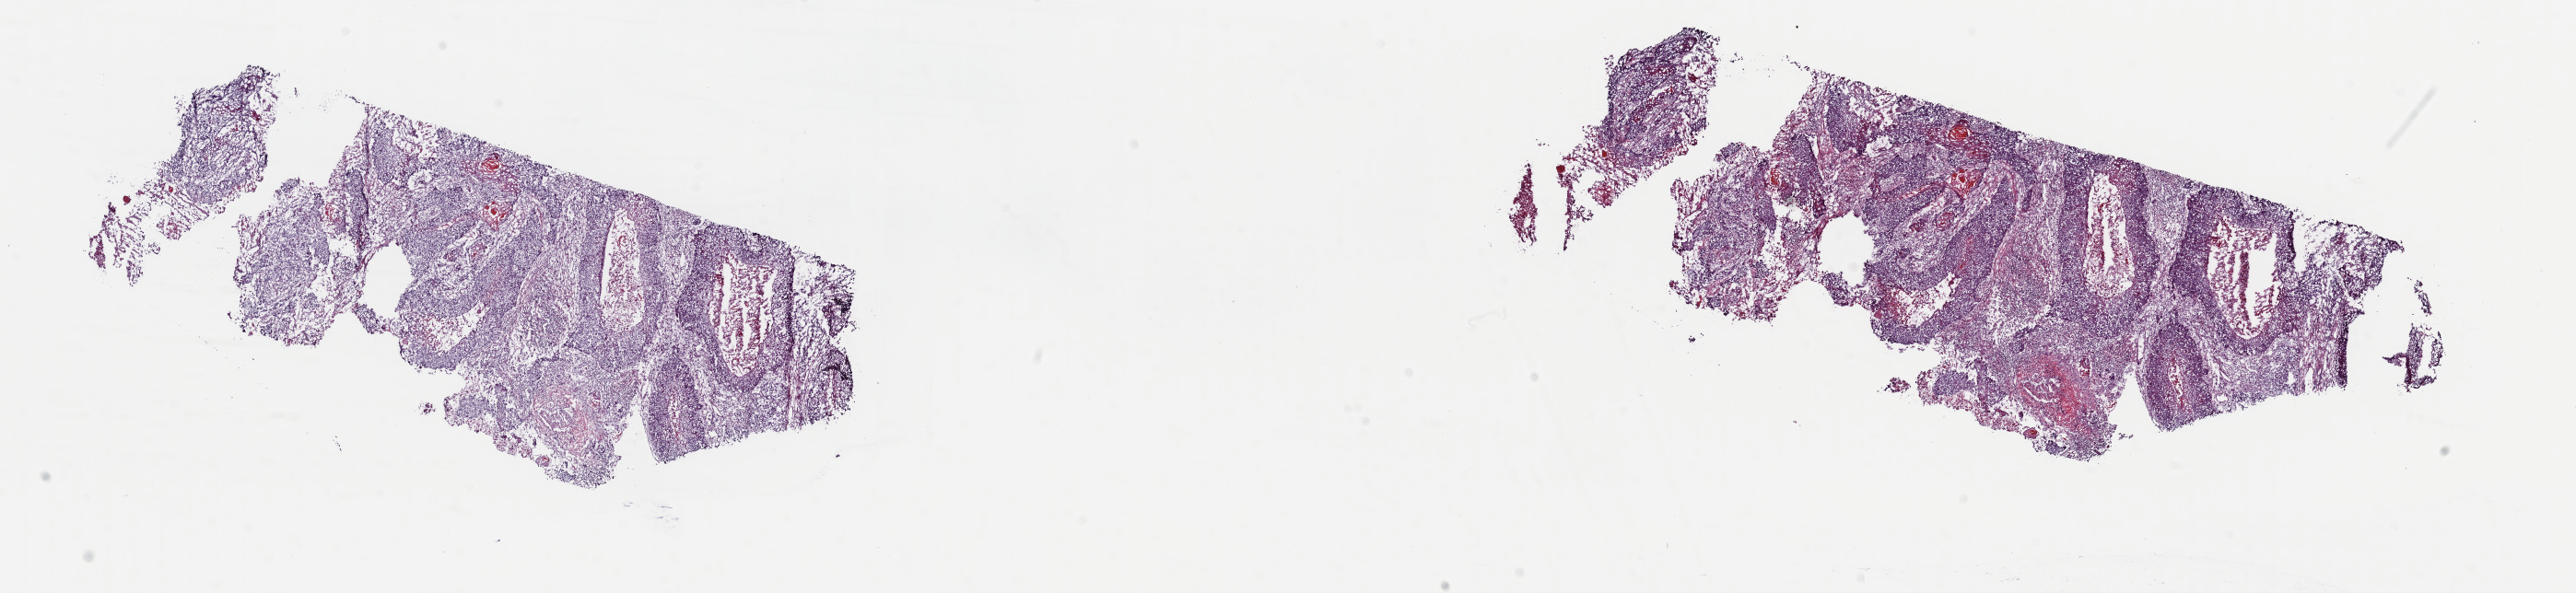
Whole-slide histology image, H&E — low-resolution overview of the scanned area, about 22.1 x 5.1 mm (acquisition: 40x scan); frozen section; sample: primary tumour, lung. Male, age 62 years at initial diagnosis. Slide review estimates, as recorded: tumour cells 60%, tumour nuclei 60%, normal cells 0%, stromal cells 20%, necrosis 20%. Infiltration values recorded for this section: lymphocyte infiltration 3%, monocyte infiltration 2%, neutrophil infiltration 3%.
Histologic diagnosis: Squamous cell carcinoma, NOS (lower lobe, lung). AJCC pathologic stage: IIB (7th edition). Laterality: left.